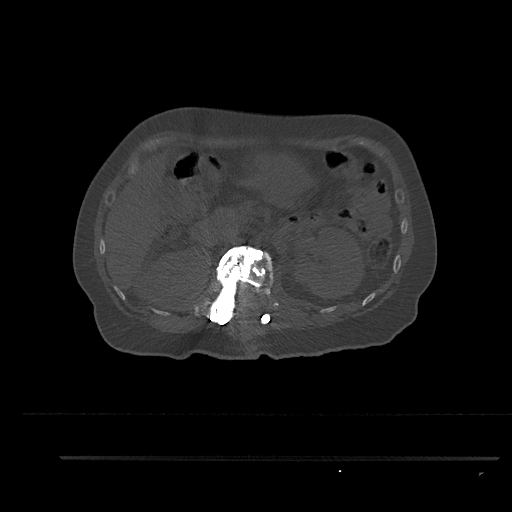
CT including the spine, one axial slice; slice 220 of 797 in the series (ordered by position); reconstruction kernel Br40s/3; bone window (W 1800 / L 400 HU); 0.5 mm slice thickness; 512 × 512 image matrix, field of view 408 × 408 mm. Patient: female, 44 years. Case-level facts recorded for this patient, not image findings: primary cancer: renal.
Structures marked on this image (semi-automatically segmented with operator editing):
- L1 vertebra: box from (x=207, y=246) to (x=275, y=324) px